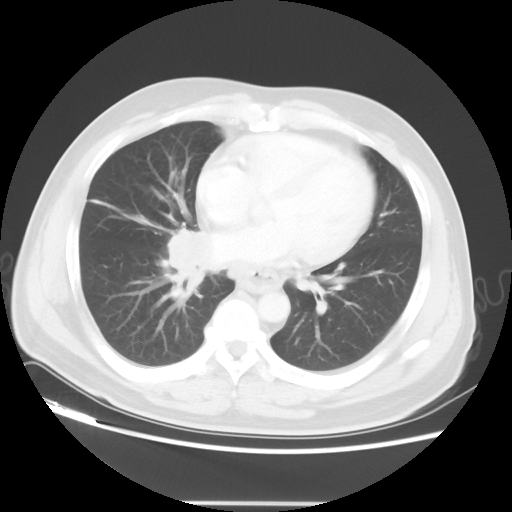
Chest CT, one axial slice. Slice 21 of 48 in the series (ordered by position). Reconstruction kernel STANDARD. Lung window (W 1500 / L -600 HU). 512 × 512 image matrix, field of view 390 × 390 mm. Male patient, age 53 years. Case-level facts recorded for this patient, not image findings: clinical TNM (as recorded): T2 N3 M0; histopathological grade: G3.
Outlined on this slice (rectangle marked by the reading radiologist):
- lung tumour (recorded histology: small cell carcinoma): box from (x=155, y=223) to (x=214, y=306) px